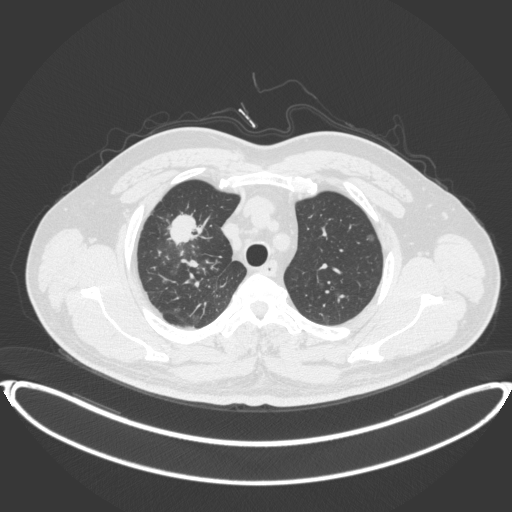
Chest CT, one axial slice; slice 310 of 399 in the series (ordered by position); reconstruction kernel B31f; 120 kVp; lung window (W 1500 / L -600 HU); 1 mm slice thickness; 512 × 512 image matrix, field of view 445 × 445 mm. Patient: male, 53 years. From the clinical record (not read from this slice): clinical TNM (as recorded): T2a N0 M0.
Annotated regions visible in this slice (bounding box drawn by a radiologist):
- lung tumour (recorded histology: adenocarcinoma): bounding box [x1, y1, x2, y2] px = [165, 211, 212, 247]